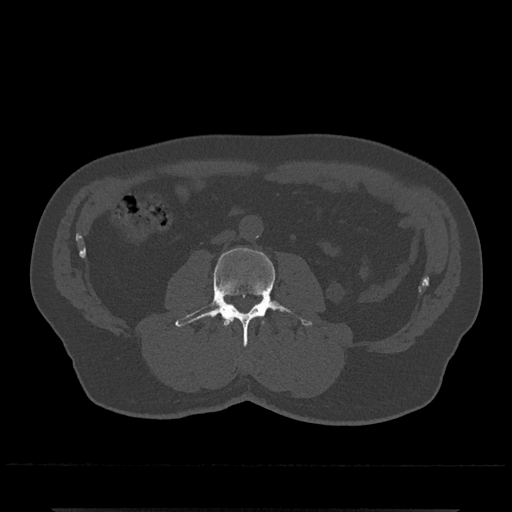
CT including the spine, one axial slice. Slice 223 of 797 in the series (ordered by position). Bone window (W 1800 / L 400 HU). 0.5 mm slice thickness. 512 × 512 image matrix. Male patient, age 67 years. Case-level facts recorded for this patient, not image findings: primary cancer: prostate.
Annotated regions visible in this slice (semi-automatically segmented with operator editing):
- L2 vertebra: bounding box (x1, y1, x2, y2) in pixels: (224, 318, 232, 326)
- L3 vertebra: (175, 248, 312, 347)